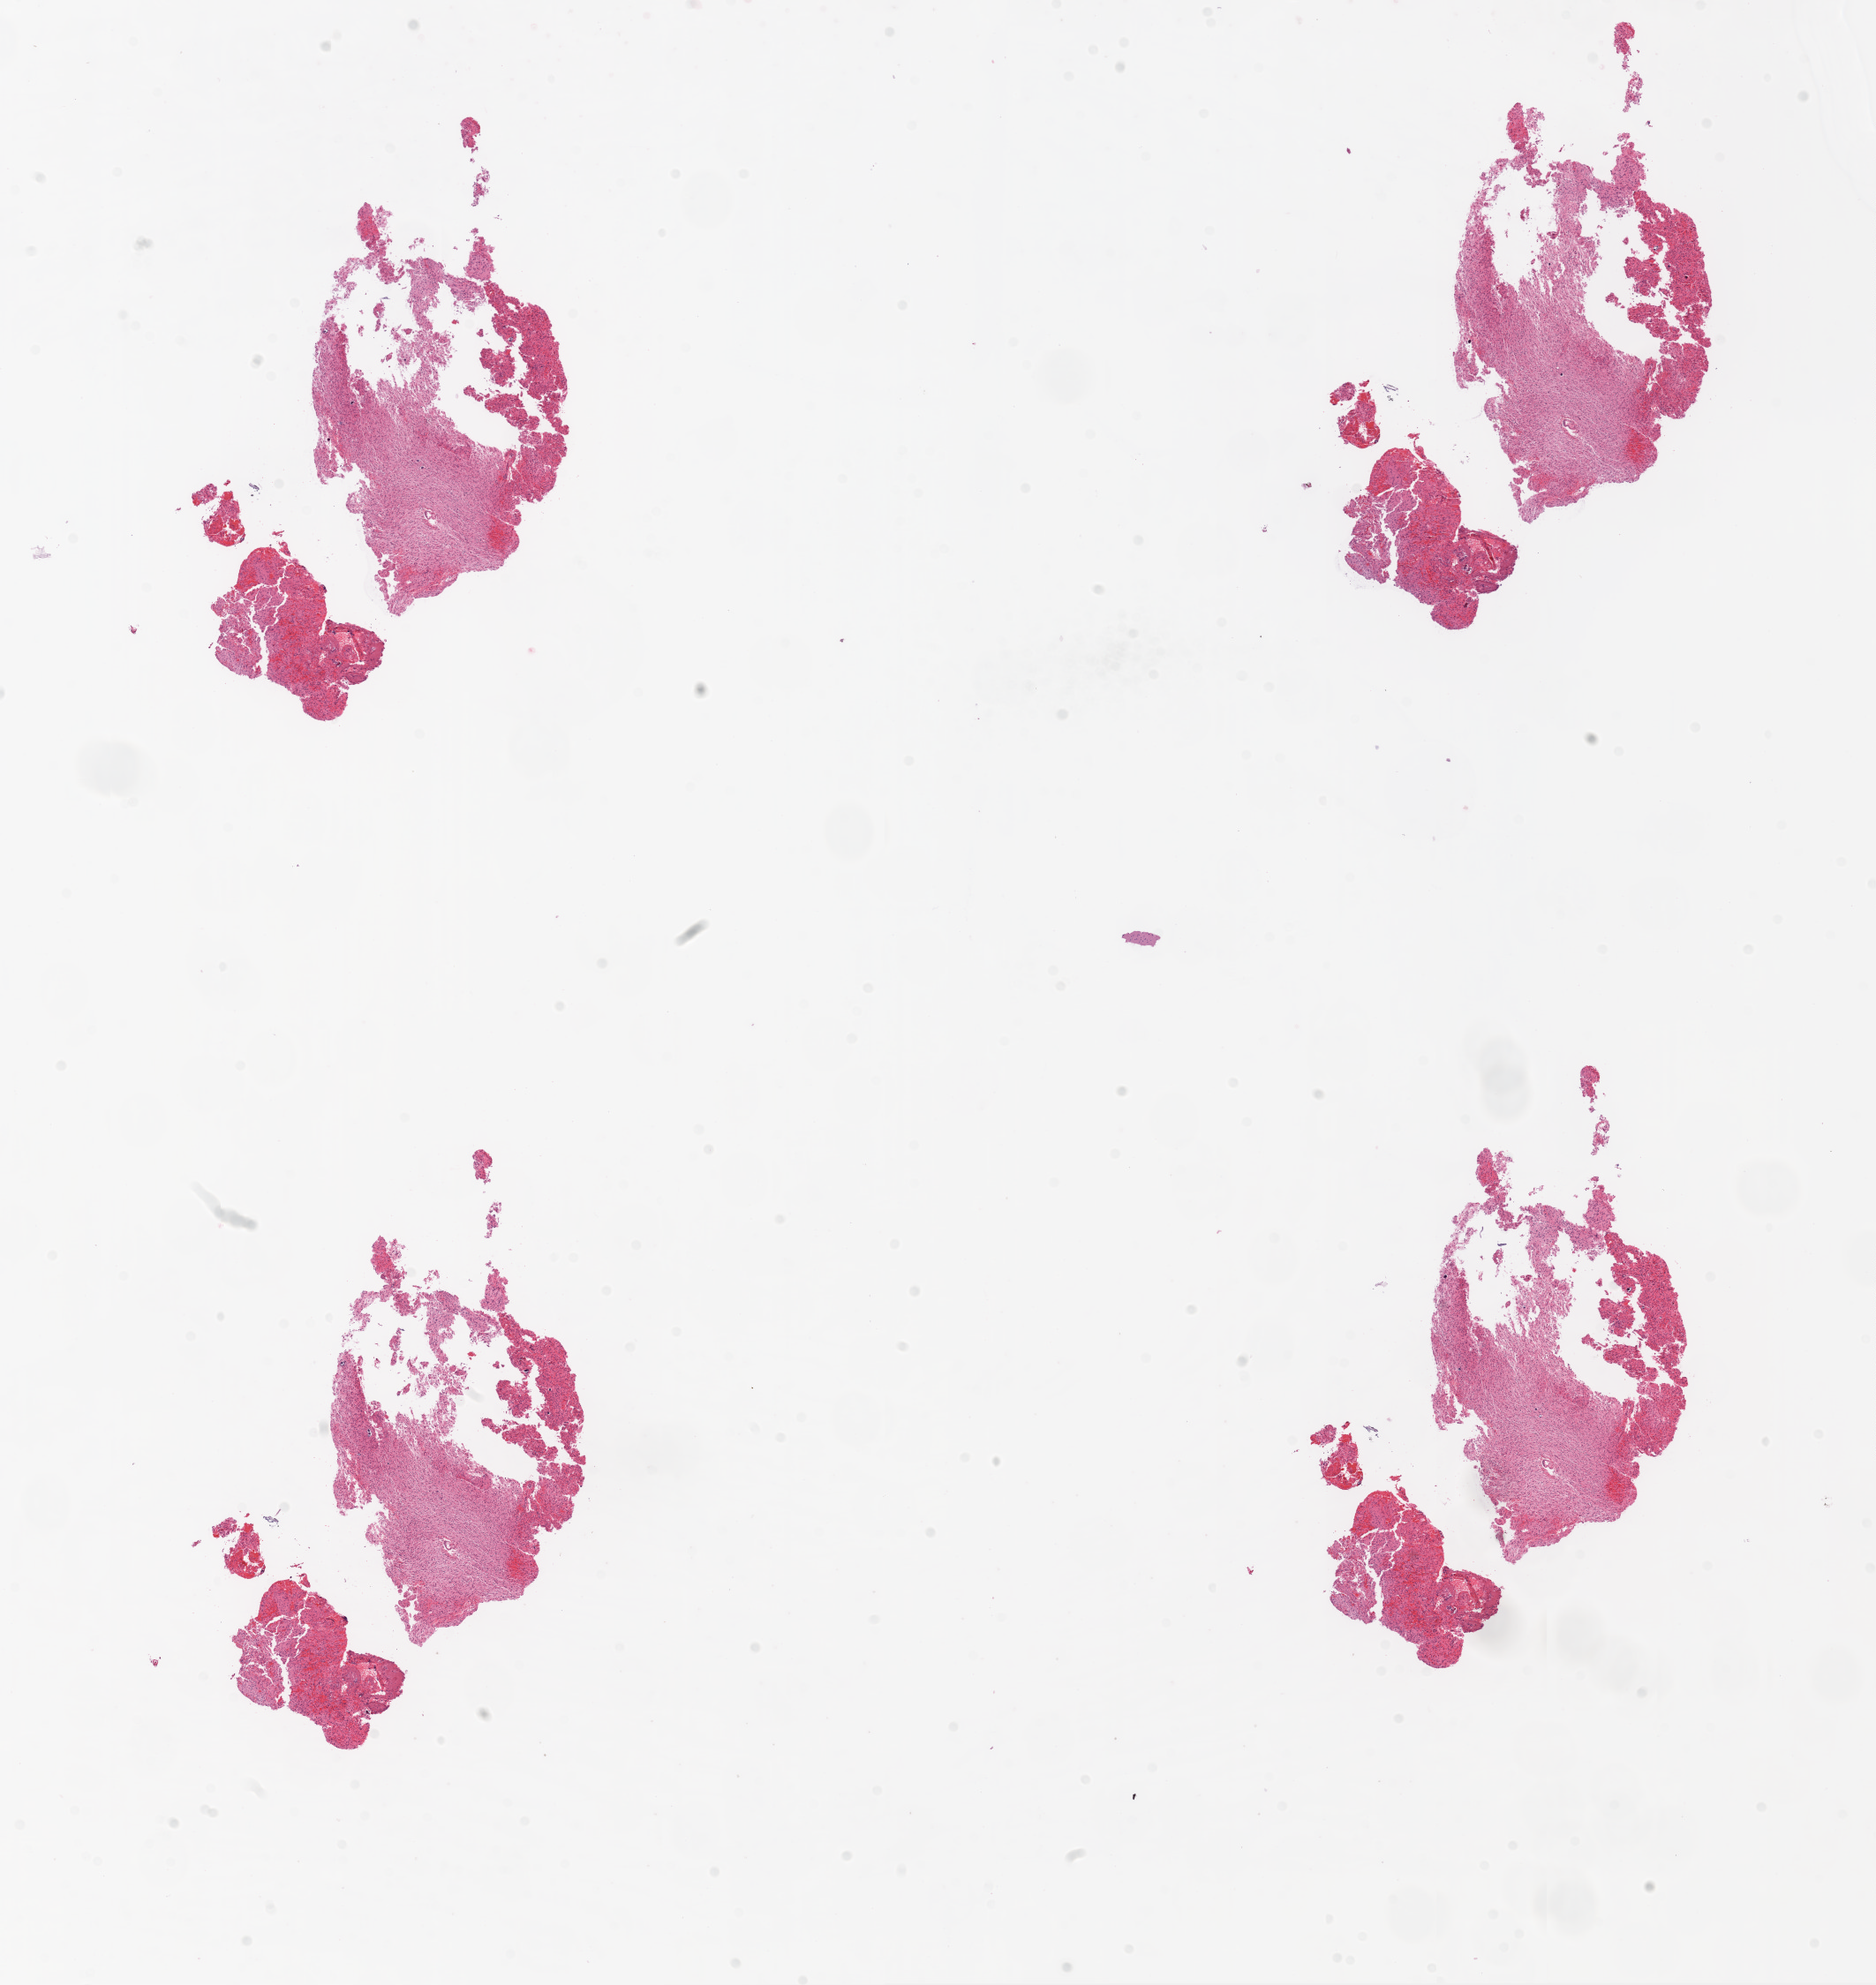
Whole-slide histology image, H&E-stained, a low-resolution overview of the entire scanned area, about 17.1 x 18.0 mm (slide scanned at 20x); formalin-fixed paraffin-embedded (FFPE) diagnostic section; primary tumour sample from the brain. Male, age 50 years at initial diagnosis.
Pathologic diagnosis: Glioblastoma.